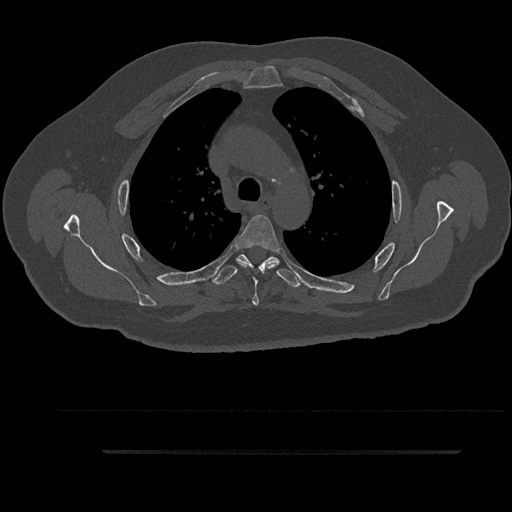
CT including the spine, one axial slice; position 655 of 797 along the scan axis; 120 kVp; bone window (W 1800 / L 400 HU); 0.5 mm slice thickness; 512 × 512 image matrix, field of view 432 × 432 mm. Male patient, age 63 years. Case-level facts recorded for this patient, not image findings: primary cancer: renal; vertebrae with lytic lesions (as recorded): T8.
Annotated regions visible in this slice (semi-automatic segmentation, software-assisted and operator-edited):
- T3 vertebra: bounding box <236,260,298,278> (left, top, right, bottom; pixels)
- T4 vertebra: <235,215,280,305>
- T5 vertebra: <213,254,301,288>